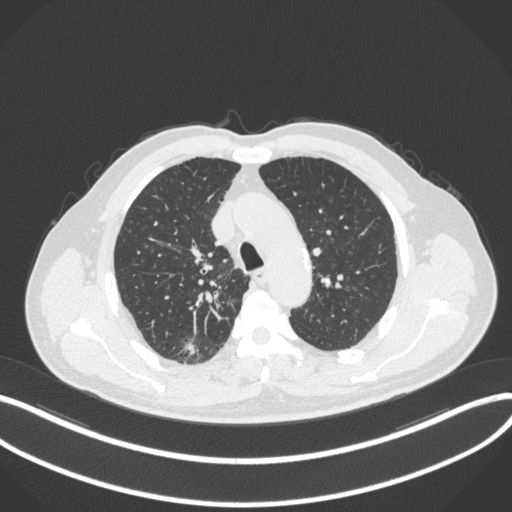
Chest CT, one axial slice; slice 275 of 366 in the series (ordered by position); reconstruction kernel B31f; lung window (W 1500 / L -600 HU); 1 mm slice thickness; 512 × 512 image matrix, field of view 400 × 400 mm. Patient: male, 69 years. From the clinical record (not read from this slice): clinical TNM (as recorded): T1b N0 M0; histopathological grade: G2-3.
Structures marked on this image (rectangle marked by the reading radiologist):
- lung tumour (recorded histology: adenocarcinoma): bounding box [x1, y1, x2, y2] px = [178, 335, 198, 359]